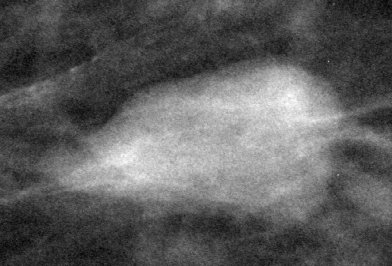
Crop from a digitized film mammogram around one marked abnormality, left breast, CC view.
Mass, shape oval, margins circumscribed; BI-RADS assessment category 2; pathology result (as recorded, not read from the image): benign.